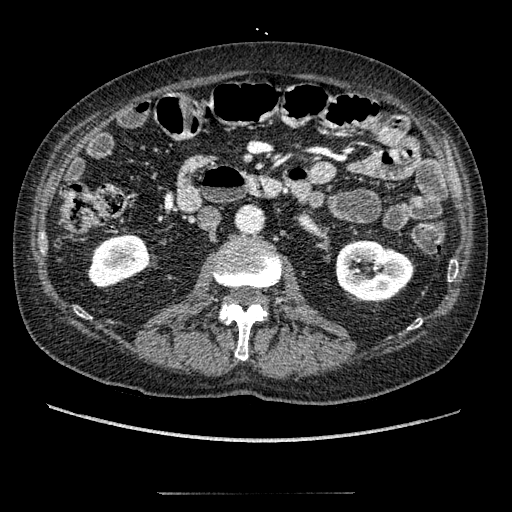
Contrast-enhanced abdominal CT, one axial slice. Slice 75 of 274 in the series (ordered by position). Reconstruction kernel STANDARD. Intravenous contrast given. Soft-tissue window (W 400 / L 40 HU). 1.25 mm slice thickness. 512 × 512 image matrix, field of view 381 × 381 mm. Male patient, age 69 years. From the clinical record (not read from this slice): diagnosis: adrenocortical carcinoma; tumour side: left adrenal; tumour size at pathology: 6.1 cm; Ki-67 index: 10 %; stage (as recorded): 3.
Structures marked on this image (semi-automatic segmentation, software-assisted and operator-edited):
- mass: box from (x=312, y=194) to (x=322, y=205) px